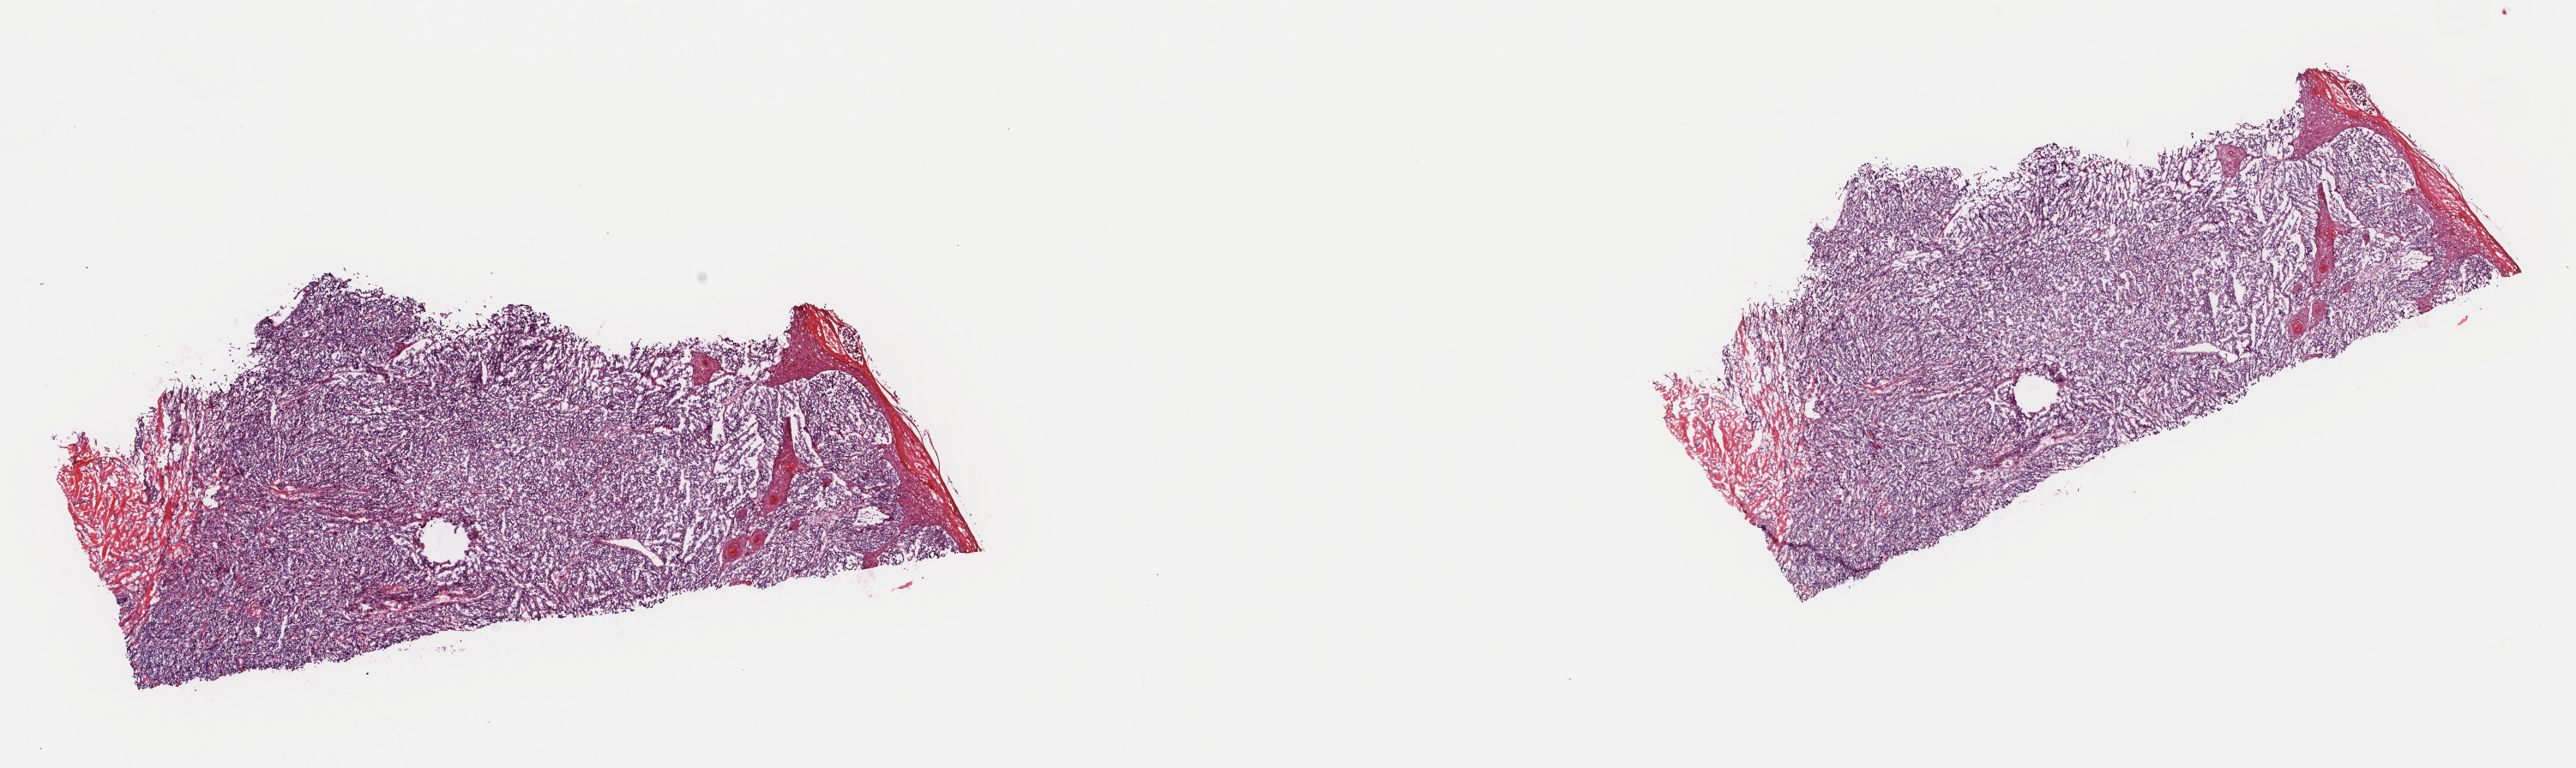
Digitized Hematoxylin and eosin (H&E) stained tissue section (whole slide), whole scanned area (about 23.7 x 7.1 mm) shown as a low-resolution overview; frozen section from the top of the tissue portion; skin, primary tumour sample. Male patient; age at initial diagnosis 71 years. Pathologist review of this section (percent, as recorded): tumour cells 75%, tumour nuclei 80%, normal cells 7%, stromal cells 13%, necrosis 5%. Inflammatory infiltration, as recorded: lymphocyte infiltration 3%, monocyte infiltration 0%, neutrophil infiltration 0%.
Histologic diagnosis: Malignant melanoma, NOS. AJCC pathologic stage: IIC (7th edition).